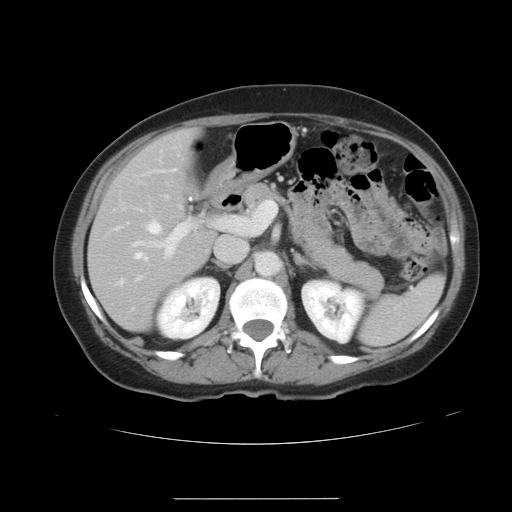
Contrast-enhanced abdominal CT, one axial slice. Slice 21 of 41 in the series (ordered by position). 120 kVp. Soft-tissue window (W 400 / L 40 HU). 5 mm slice thickness. 512 × 512 image matrix. Female patient, age 63 years. From the clinical record (not read from this slice): diagnosis: colorectal cancer liver metastases, imaged before liver resection; multiple liver metastases: yes; largest metastasis: 1.5 cm; chemotherapy before resection: no.
Annotated regions visible in this slice (expert manual segmentation):
- hepatic veins: box from (x=119, y=169) to (x=174, y=284) px
- liver: (x=90, y=131)–(x=216, y=331)
- planned liver remnant (the part of the liver to remain after resection): (x=90, y=131)–(x=216, y=331)
- portal vein (with intrahepatic branches): (x=134, y=223)–(x=188, y=280)